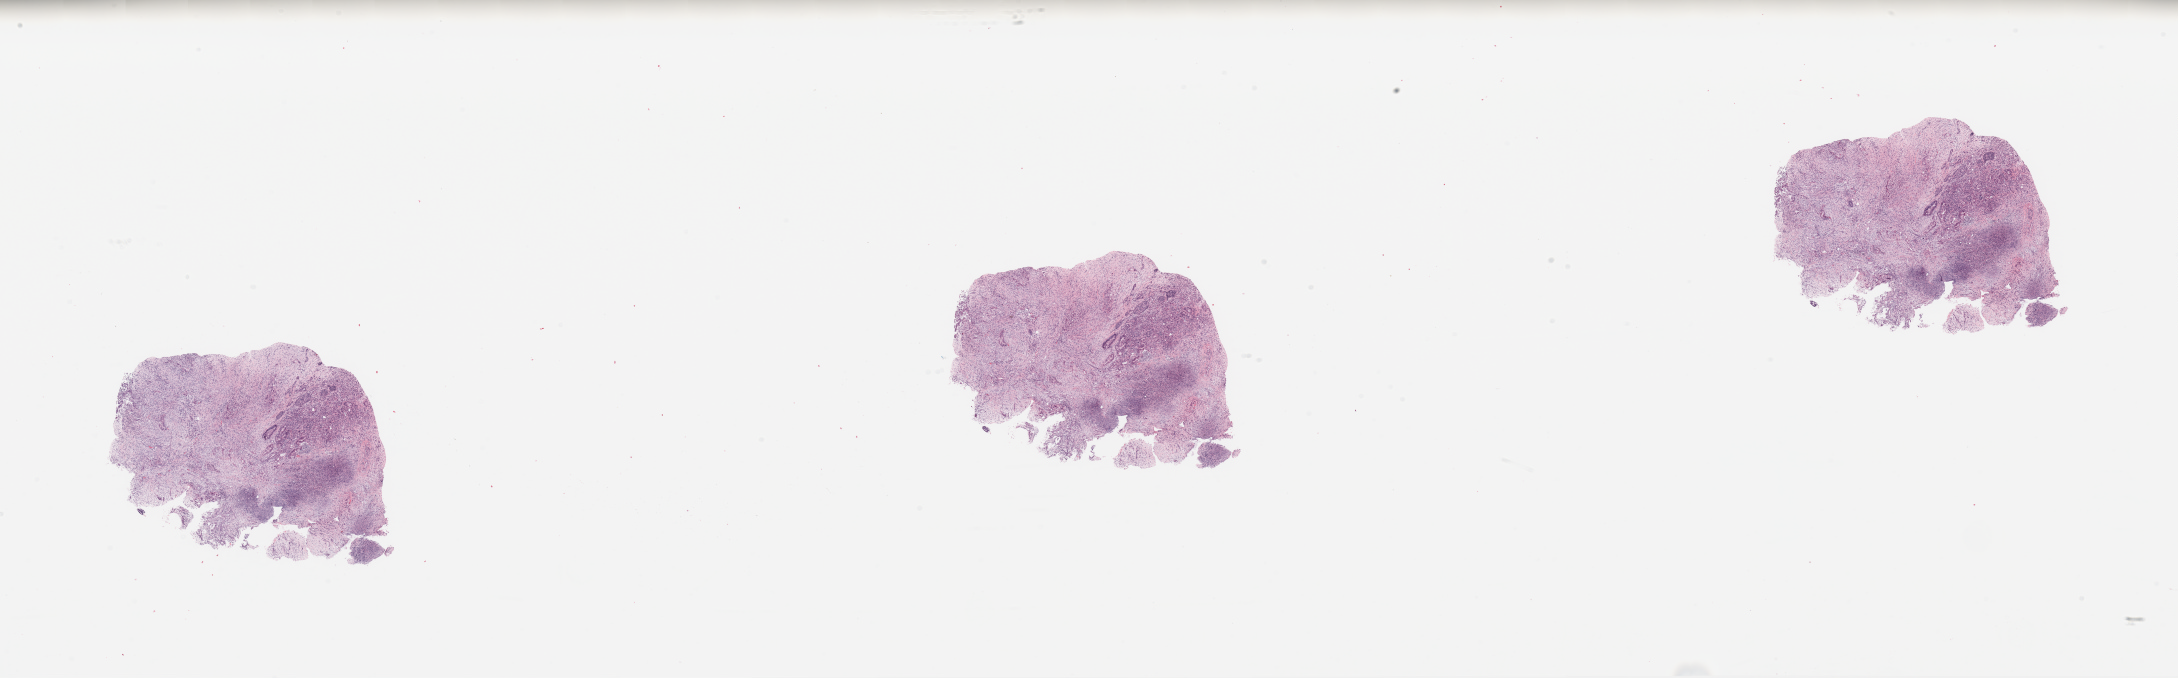
H&E whole-slide image, shown as a low-resolution overview of the whole scanned area (about 34.5 x 10.7 mm, from a 20x scan). Tumour tissue sample, sampled site: pancreas. Female, 68 y/o. Histologic grade: G2 (moderately differentiated). Pathologist review of this section (percent, as recorded): tumour nuclei 25%, necrosis 20%.
* AJCC pathologic stage: IIB
* diagnosis: Infiltrating duct carcinoma, NOS
* primary tumour site (as recorded): head